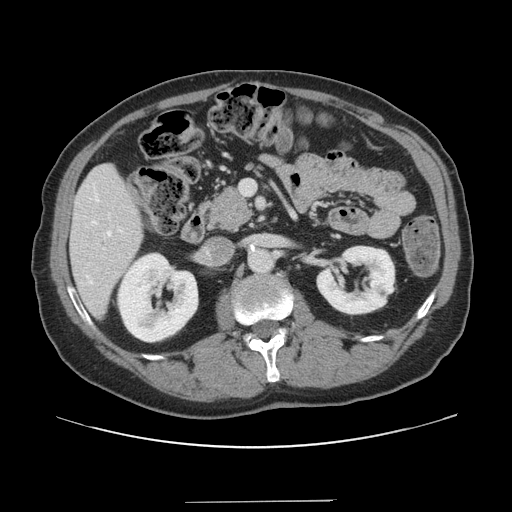
Contrast-enhanced abdominal CT, one axial slice. Slice 64 of 151 in the series (ordered by position). 120 kVp. Intravenous contrast given. Soft-tissue window (W 400 / L 40 HU). 512 × 512 image matrix, field of view 399 × 399 mm. Male patient, age 63 years. From the clinical record (not read from this slice): diagnosis: colorectal cancer liver metastases, imaged before liver resection; multiple liver metastases: no; largest metastasis: 2.1 cm; disease in both lobes: no.
Annotated regions visible in this slice (expert manual segmentation):
- hepatic veins: bounding box <89,231,111,284> (left, top, right, bottom; pixels)
- liver: <72,165,143,316>
- planned liver remnant (the part of the liver to remain after resection): <72,166,143,317>
- portal vein (with intrahepatic branches): <103,180,255,250>